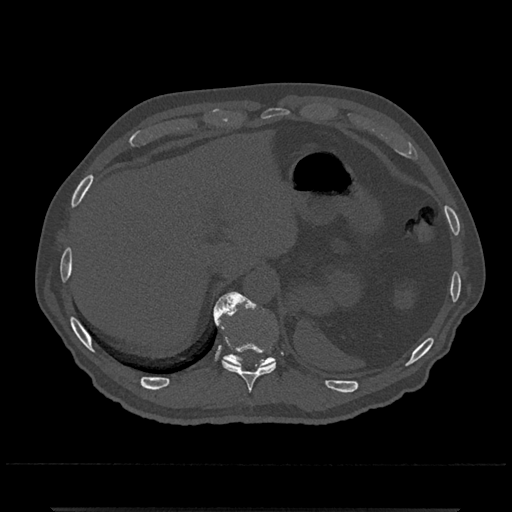
CT including the spine, one axial slice; position 533 of 797 along the scan axis; 120 kVp; bone window (W 1800 / L 400 HU); 0.5 mm slice thickness; 512 × 512 image matrix, field of view 393 × 393 mm. Patient: male, 67 years. From the clinical record (not read from this slice): primary cancer: prostate.
Annotated regions visible in this slice (semi-automatically segmented with operator editing):
- T10 vertebra: bounding box <215,292,276,404> (left, top, right, bottom; pixels)
- T11 vertebra: <213,293,276,367>